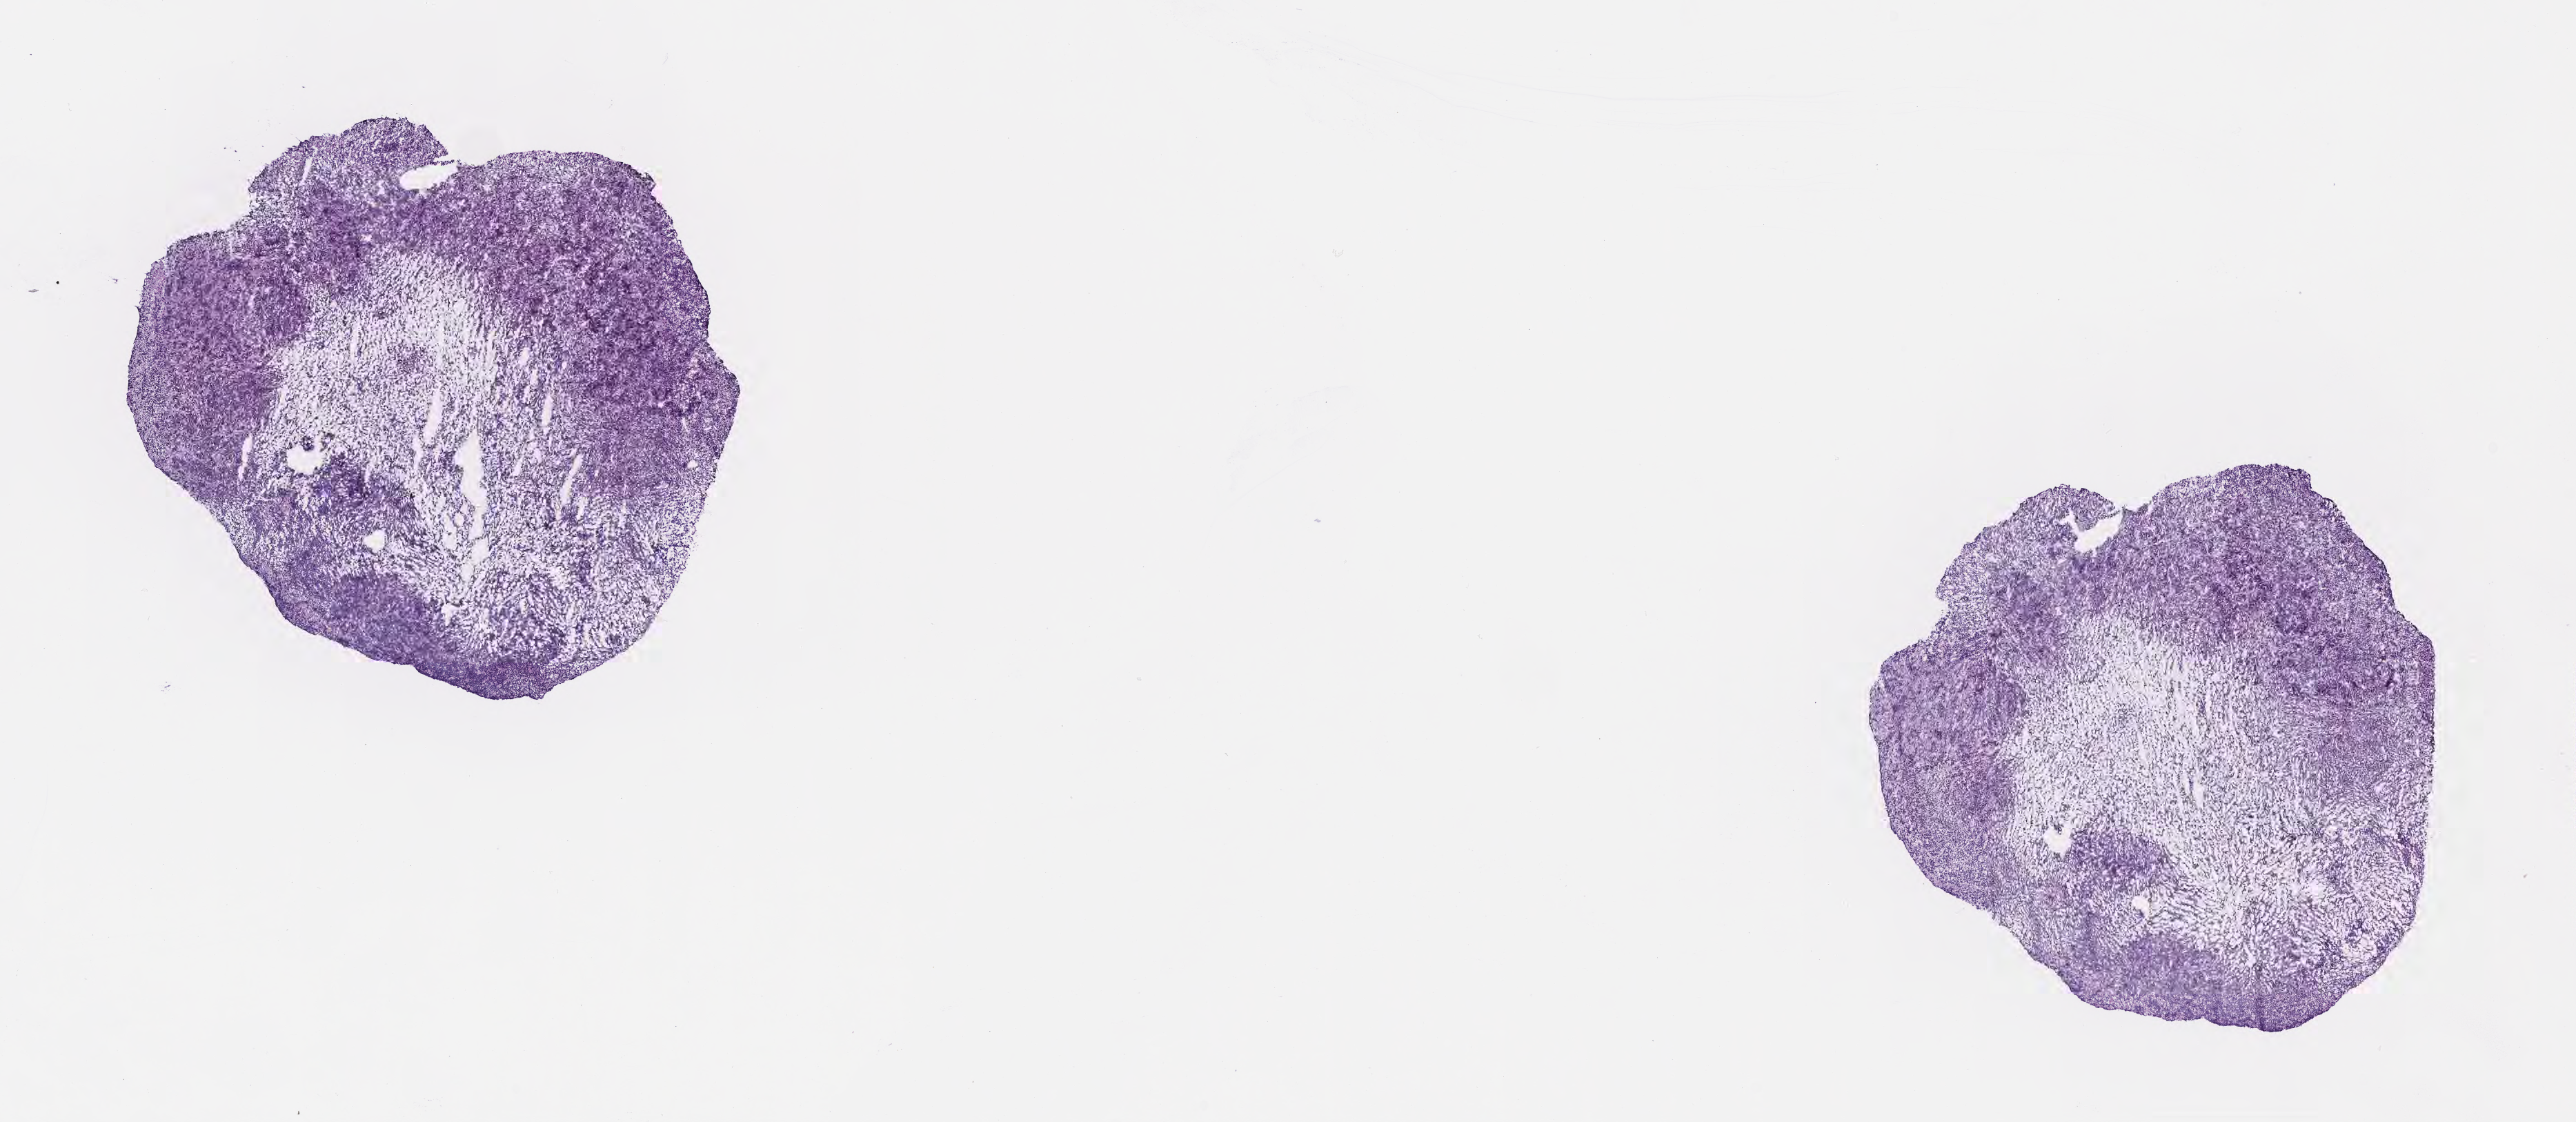
Digitized H&E-stained section, a low-resolution overview of the entire scanned area, about 15.1 x 6.6 mm. Frozen section. Specimen: primary tumor. Male patient; age at initial diagnosis 5 years. Slide review estimates, as recorded: tumor cells 60%, tumor nuclei 85%, stromal cells 30%, necrosis 10%, normal cells 0%. Infiltration values recorded for this section: lymphocyte infiltration 35%, monocyte infiltration 20%, neutrophil infiltration 5%.
Histologic diagnosis: Burkitt lymphoma, NOS. Ann Arbor stage (patient): Stage II.